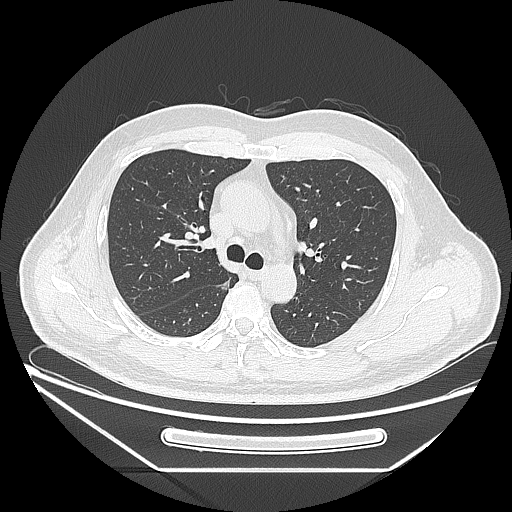
Chest CT, one axial slice. Position 169 of 271 along the scan axis. 120 kVp. Lung window (W 1500 / L -600 HU). 1.25 mm slice thickness. 512 × 512 image matrix, field of view 414 × 414 mm. Male patient, age 49 years. From the clinical record (not read from this slice): clinical TNM (as recorded): T1b N0 M0.
Annotated regions visible in this slice (rectangle marked by the reading radiologist):
- lung tumour (recorded histology: adenocarcinoma): box from (x=216, y=278) to (x=237, y=295) px